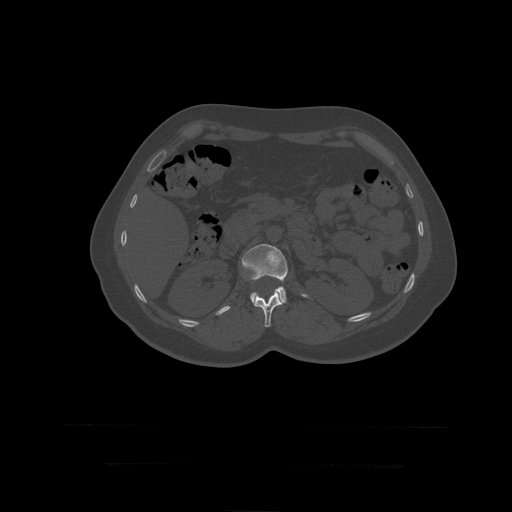
CT including the spine, one axial slice; slice 162 of 399 in the series (ordered by position); 120 kVp; bone window (W 1800 / L 400 HU); 1.25 mm slice thickness; 512 × 512 image matrix, field of view 450 × 450 mm. Patient age 41 years. Case-level facts recorded for this patient, not image findings: primary cancer: breast.
Outlined on this slice (semi-automatic segmentation, software-assisted and operator-edited):
- L1 vertebra: box from (x=252, y=291) to (x=284, y=328) px
- L2 vertebra: (x=242, y=244)–(x=308, y=304)